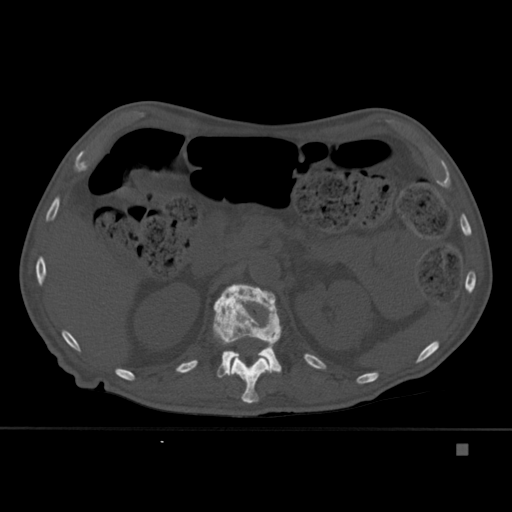
CT including the spine, one axial slice; position 191 of 451 along the scan axis; bone window (W 1800 / L 400 HU); 1.5 mm slice thickness; 512 × 512 image matrix, field of view 378 × 378 mm. Male patient, age 75 years. From the clinical record (not read from this slice): primary cancer: prostate.
Outlined on this slice (semi-automatically segmented with operator editing):
- L1 vertebra: bounding box [x1, y1, x2, y2] px = [213, 284, 282, 378]
- T12 vertebra: [230, 338, 271, 404]